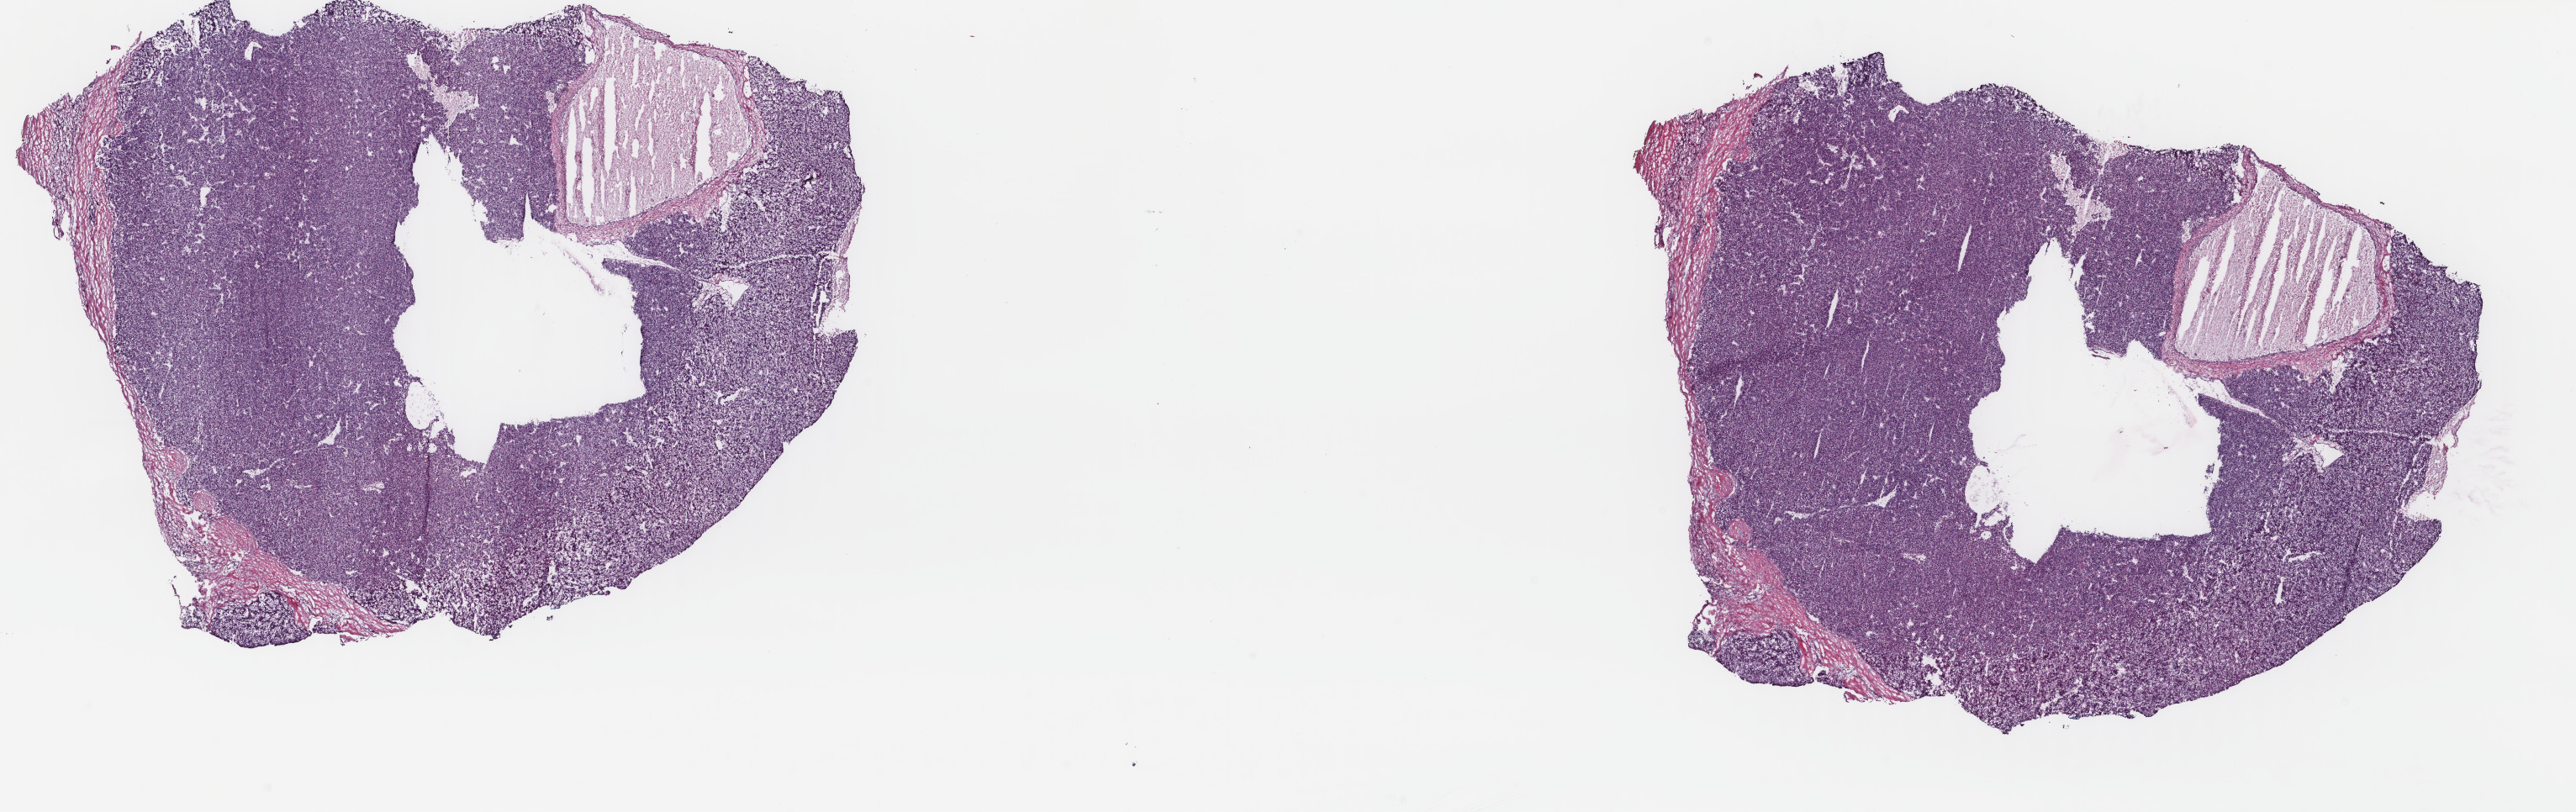
Digitized H&E-stained tissue section (whole slide), whole scanned area (about 24.3 x 7.7 mm, acquisition: 40x scan) shown as a low-resolution overview. Frozen section. Primary tumour sample from the liver. Female, age 70 years at initial diagnosis. Composition of this section per pathologist review: tumour cells 90%, tumour nuclei 95%.
Diagnosis: Hepatocellular carcinoma, NOS.